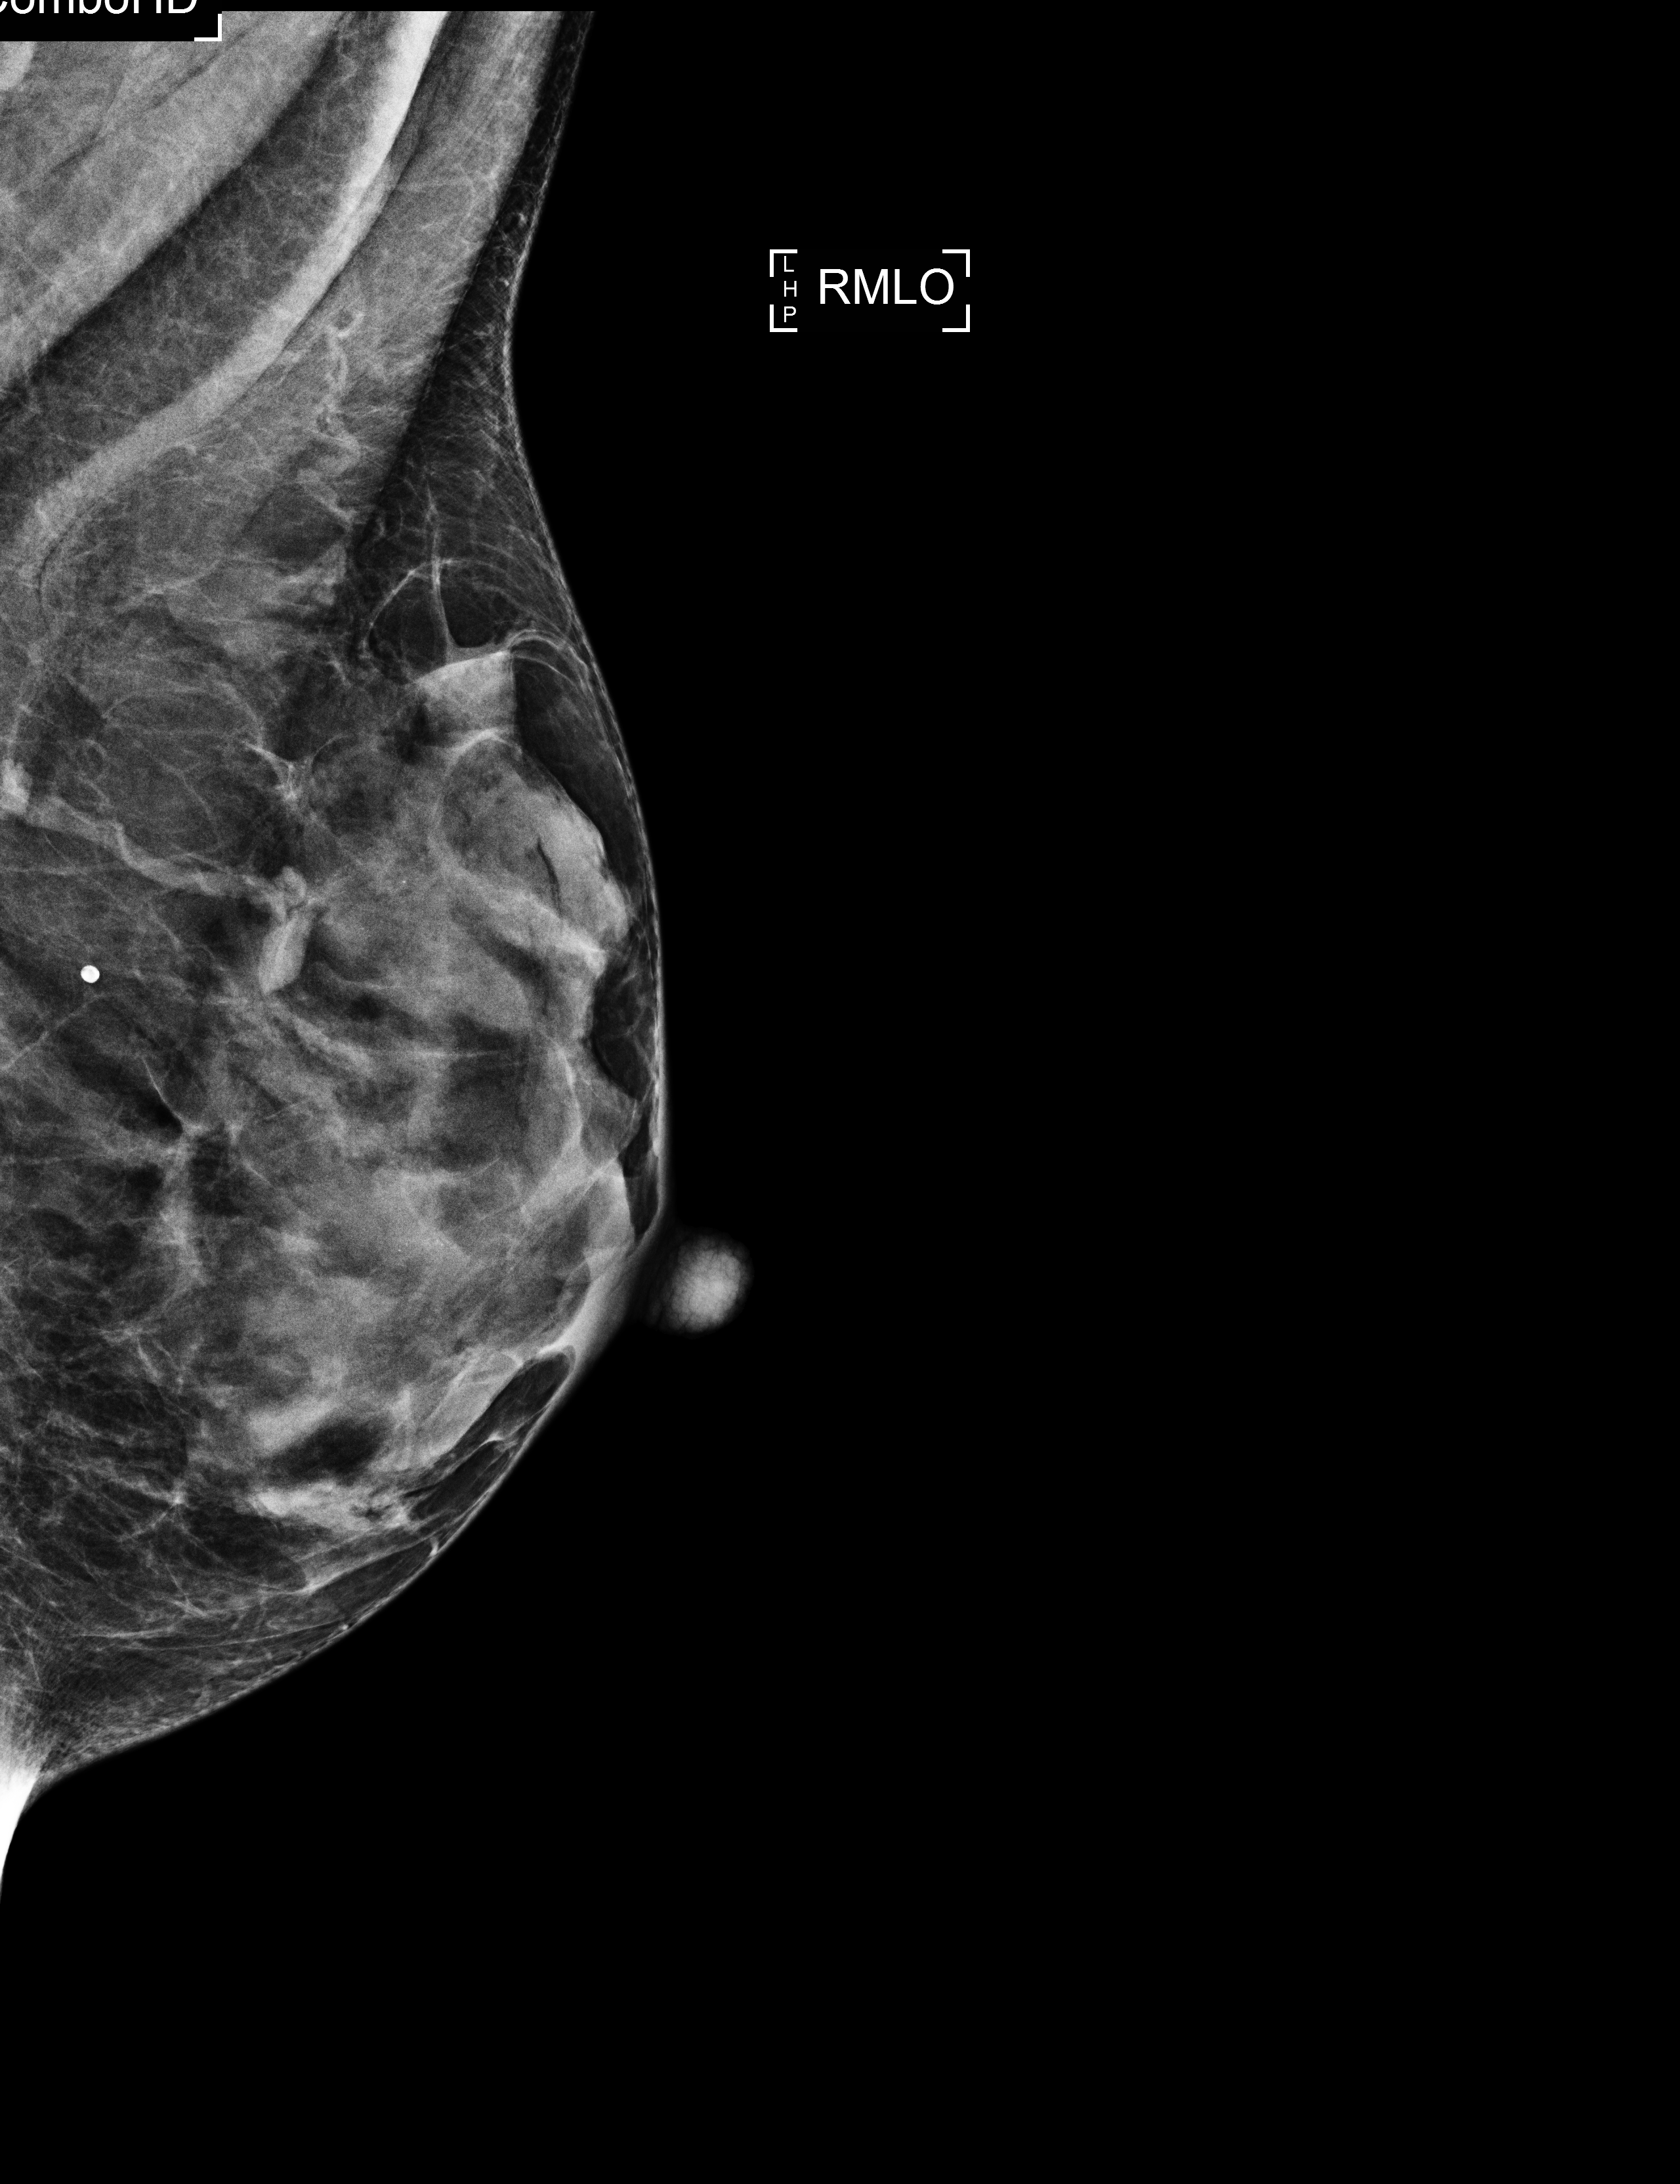
Annual screening mammography examination. Female patient, age 54 years.
Image type: full-field digital mammogram. Breast: right. Projection: MLO view.